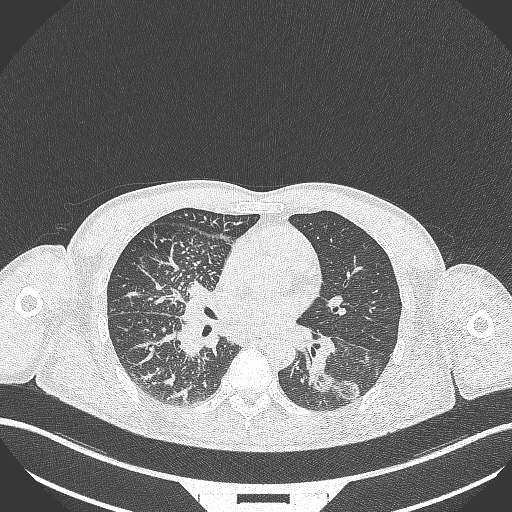
Chest CT, one axial slice; slice 157 of 348 in the series (ordered by position); reconstruction kernel B70f; lung window (W 1500 / L -600 HU); 1 mm slice thickness; 512 × 512 image matrix. Patient: male, 49 years. From the clinical record (not read from this slice): clinical TNM (as recorded): T2b N1 M0.
Structures marked on this image (rectangle marked by the reading radiologist):
- lung tumour (recorded histology: adenocarcinoma): bounding box [x1, y1, x2, y2] px = [303, 367, 365, 412]